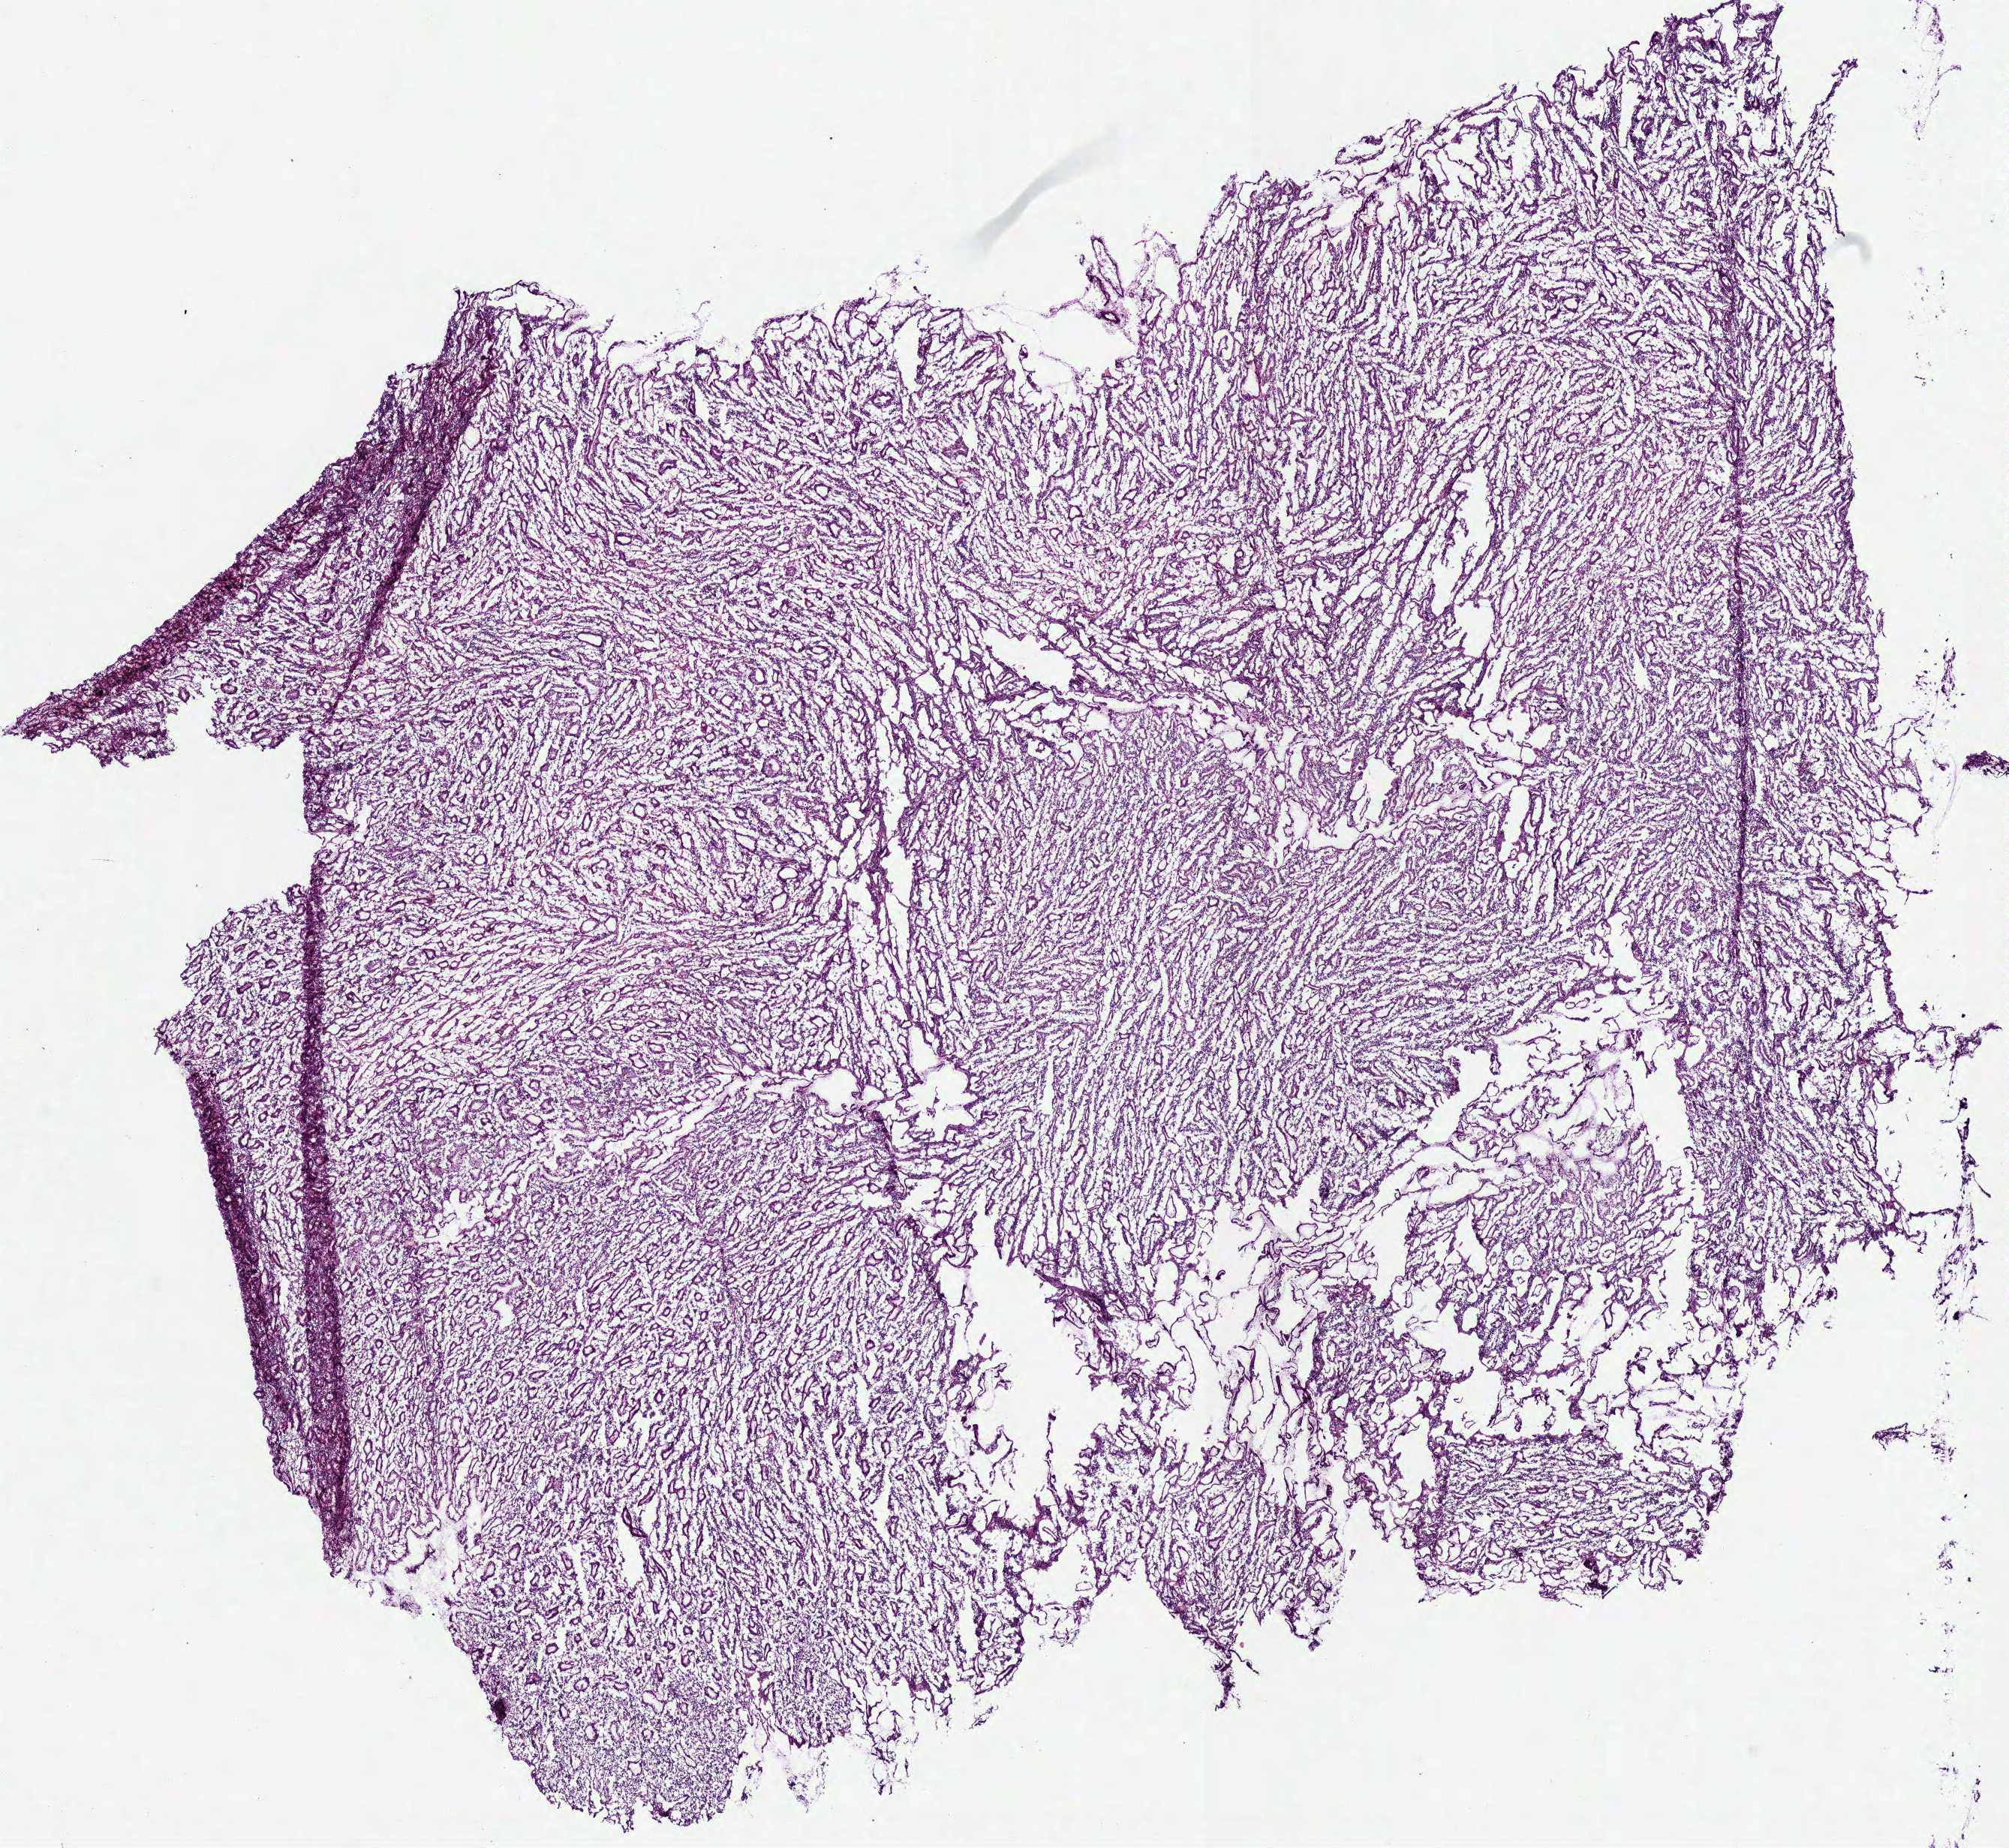
Whole-slide histology image, H&E, shown as a low-resolution overview of the whole scanned area (about 10.5 x 9.7 mm, from a 40x scan); frozen section from the top of the tissue portion; sample: solid tissue normal (non-tumour tissue), stomach. Female, age 64 years at initial diagnosis.
• this section: solid tissue normal (non-tumour) sample from the same patient
• patient diagnosis: Adenocarcinoma, NOS (cardia, NOS)